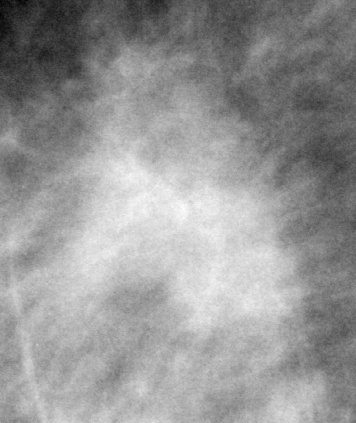
Region of interest cut from a scanned film mammogram (one marked finding), right breast, MLO view.
Mass, shape irregular, margins spiculated; BI-RADS assessment category 5; subtlety rating 5 on a 1 (subtle) to 5 (obvious) scale; pathology result (as recorded, not read from the image): malignant.